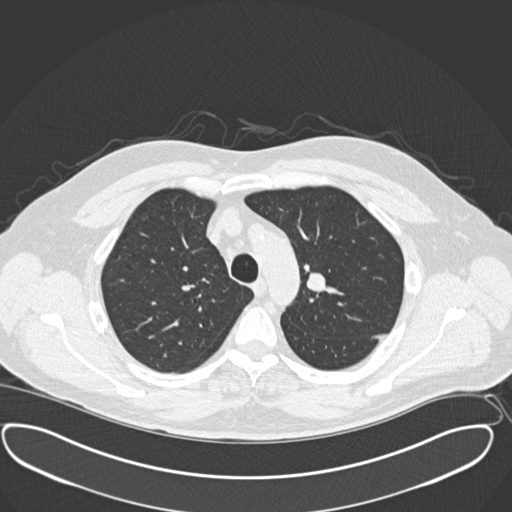
Axial slice from a low-dose chest CT screening exam. Third screening round (two years after baseline). Lung window (W 1500 / L -600 HU). 512 × 512 image matrix, field of view 416 × 416 mm. Male participant, aged 56 years at enrolment.
- Lesion marked by an expert reader, bounding box [x1, y1, x2, y2] px = [288, 262, 343, 309].
- Screening reader's record for this exam: no non-calcified nodule ≥4 mm recorded.
- Official screen result: negative screen, minor abnormalities not suspicious for lung cancer.
- Lung cancer was diagnosed 156 days after this screen: neuroendocrine carcinoma, NOS, left upper lobe, well differentiated (G1), stage IA (AJCC 6th edition), 20 mm at pathology.